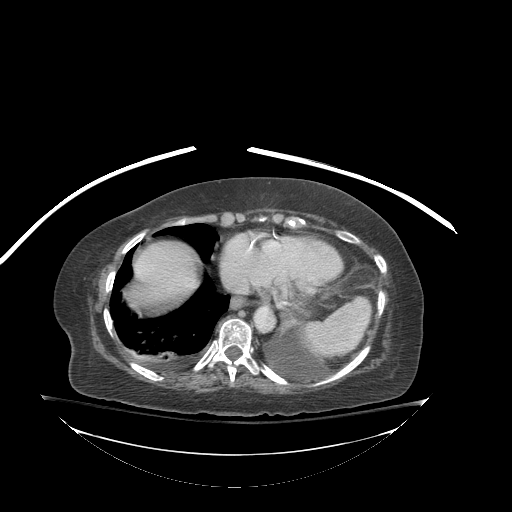
Contrast-enhanced abdominal CT (liver protocol), one axial slice. Slice 79 of 81 in the series (ordered by position). 140 kVp. Soft-tissue window (W 400 / L 40 HU). 512 × 512 image matrix, field of view 500 × 500 mm. From the clinical record (not read from this slice): diagnosis: hepatocellular carcinoma (patient treated with transarterial chemoembolisation; whether this scan precedes or follows treatment is not stated here); TNM stage (as recorded): Stage-I; Child-Pugh class: B; tumour differentiation: well-moderately differentiated; tumour nodularity: uninodular.
Outlined on this slice (semi-automatic segmentation, software-assisted and operator-edited):
- abdominal aorta: bounding box <255,307,274,329> (left, top, right, bottom; pixels)
- liver parenchyma outside the tumour (the mass and vessels are separate outlines, so this box may not span the whole liver): <126,242,198,306>
- liver vessels: <137,261,192,287>